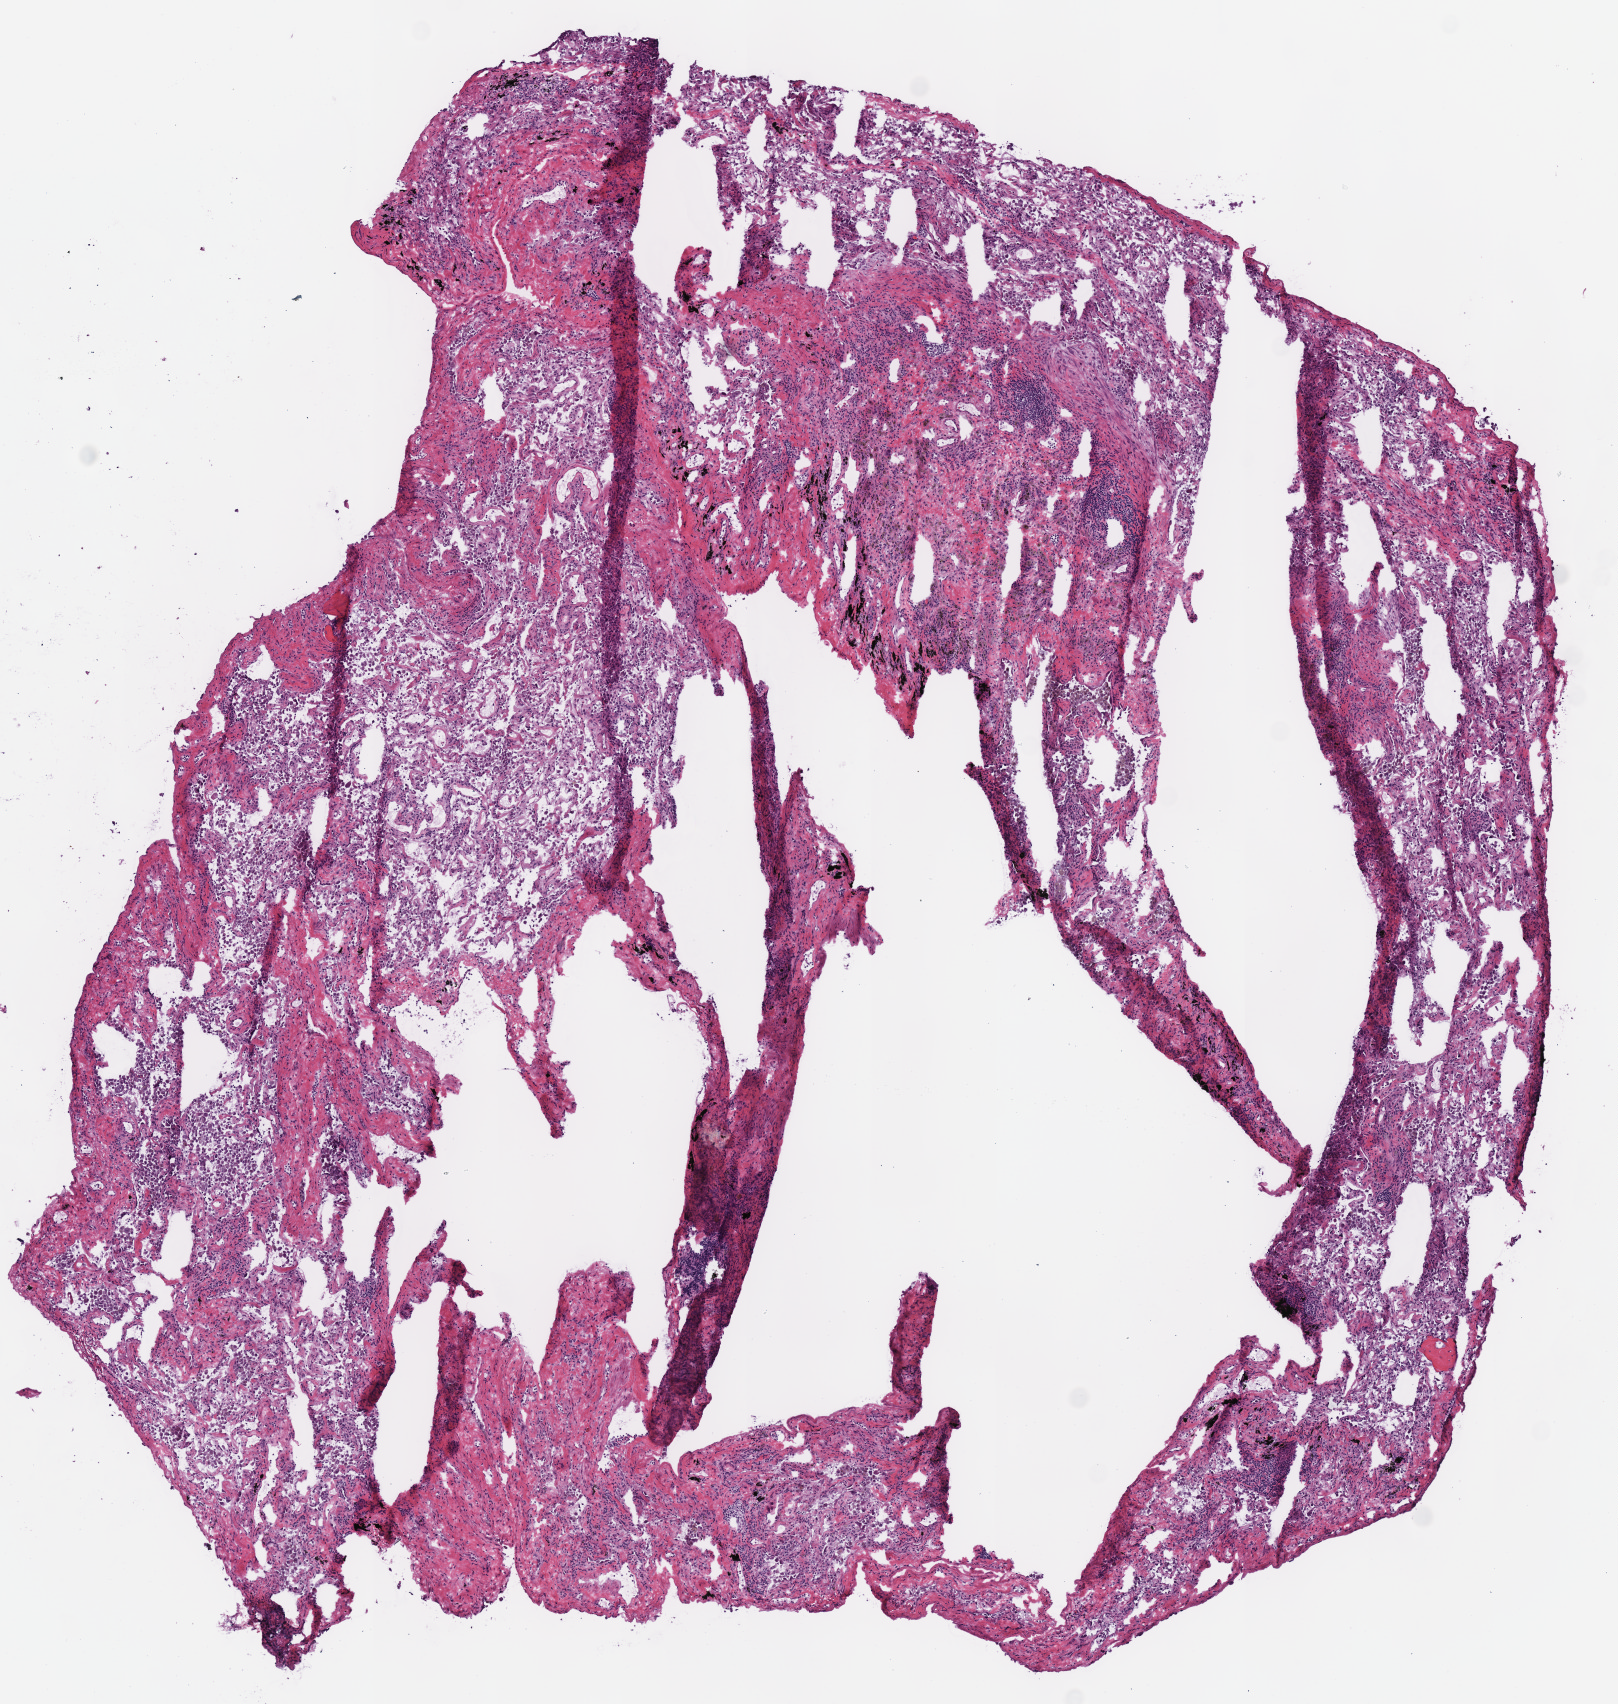
H&E-stained whole-slide image — whole scanned area (about 6.4 x 6.7 mm) shown as a low-resolution overview; frozen section; sample: solid tissue normal (non-tumour tissue), lung. Patient: male, age at initial diagnosis 62 years. Infiltration values recorded for this section: lymphocyte infiltration 20%, monocyte infiltration 20%.
- this section: solid tissue normal (non-tumour) sample from the same patient
- patient diagnosis: Adenocarcinoma with mixed subtypes (upper lobe, lung)